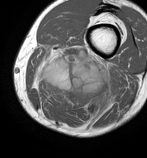
MRI of an extremity soft-tissue mass, one axial slice; position 26 of 86 along the scan axis; MR volume resampled by the dataset authors to the PET/CT grid (not the native acquisition matrix); 147 × 158 image matrix. Male patient. Case-level facts recorded for this patient, not image findings: histological type: undifferentiated pleomorphic liposarcoma; grade: high; site of the primary tumour: left thigh.
Annotated regions visible in this slice (expert contour drawn on MRI and transferred to this co-registered scan by the dataset authors):
- gross tumour volume including surrounding oedema: bounding box [x1, y1, x2, y2] px = [32, 44, 116, 125]
- gross tumour volume (mass): [44, 63, 106, 105]